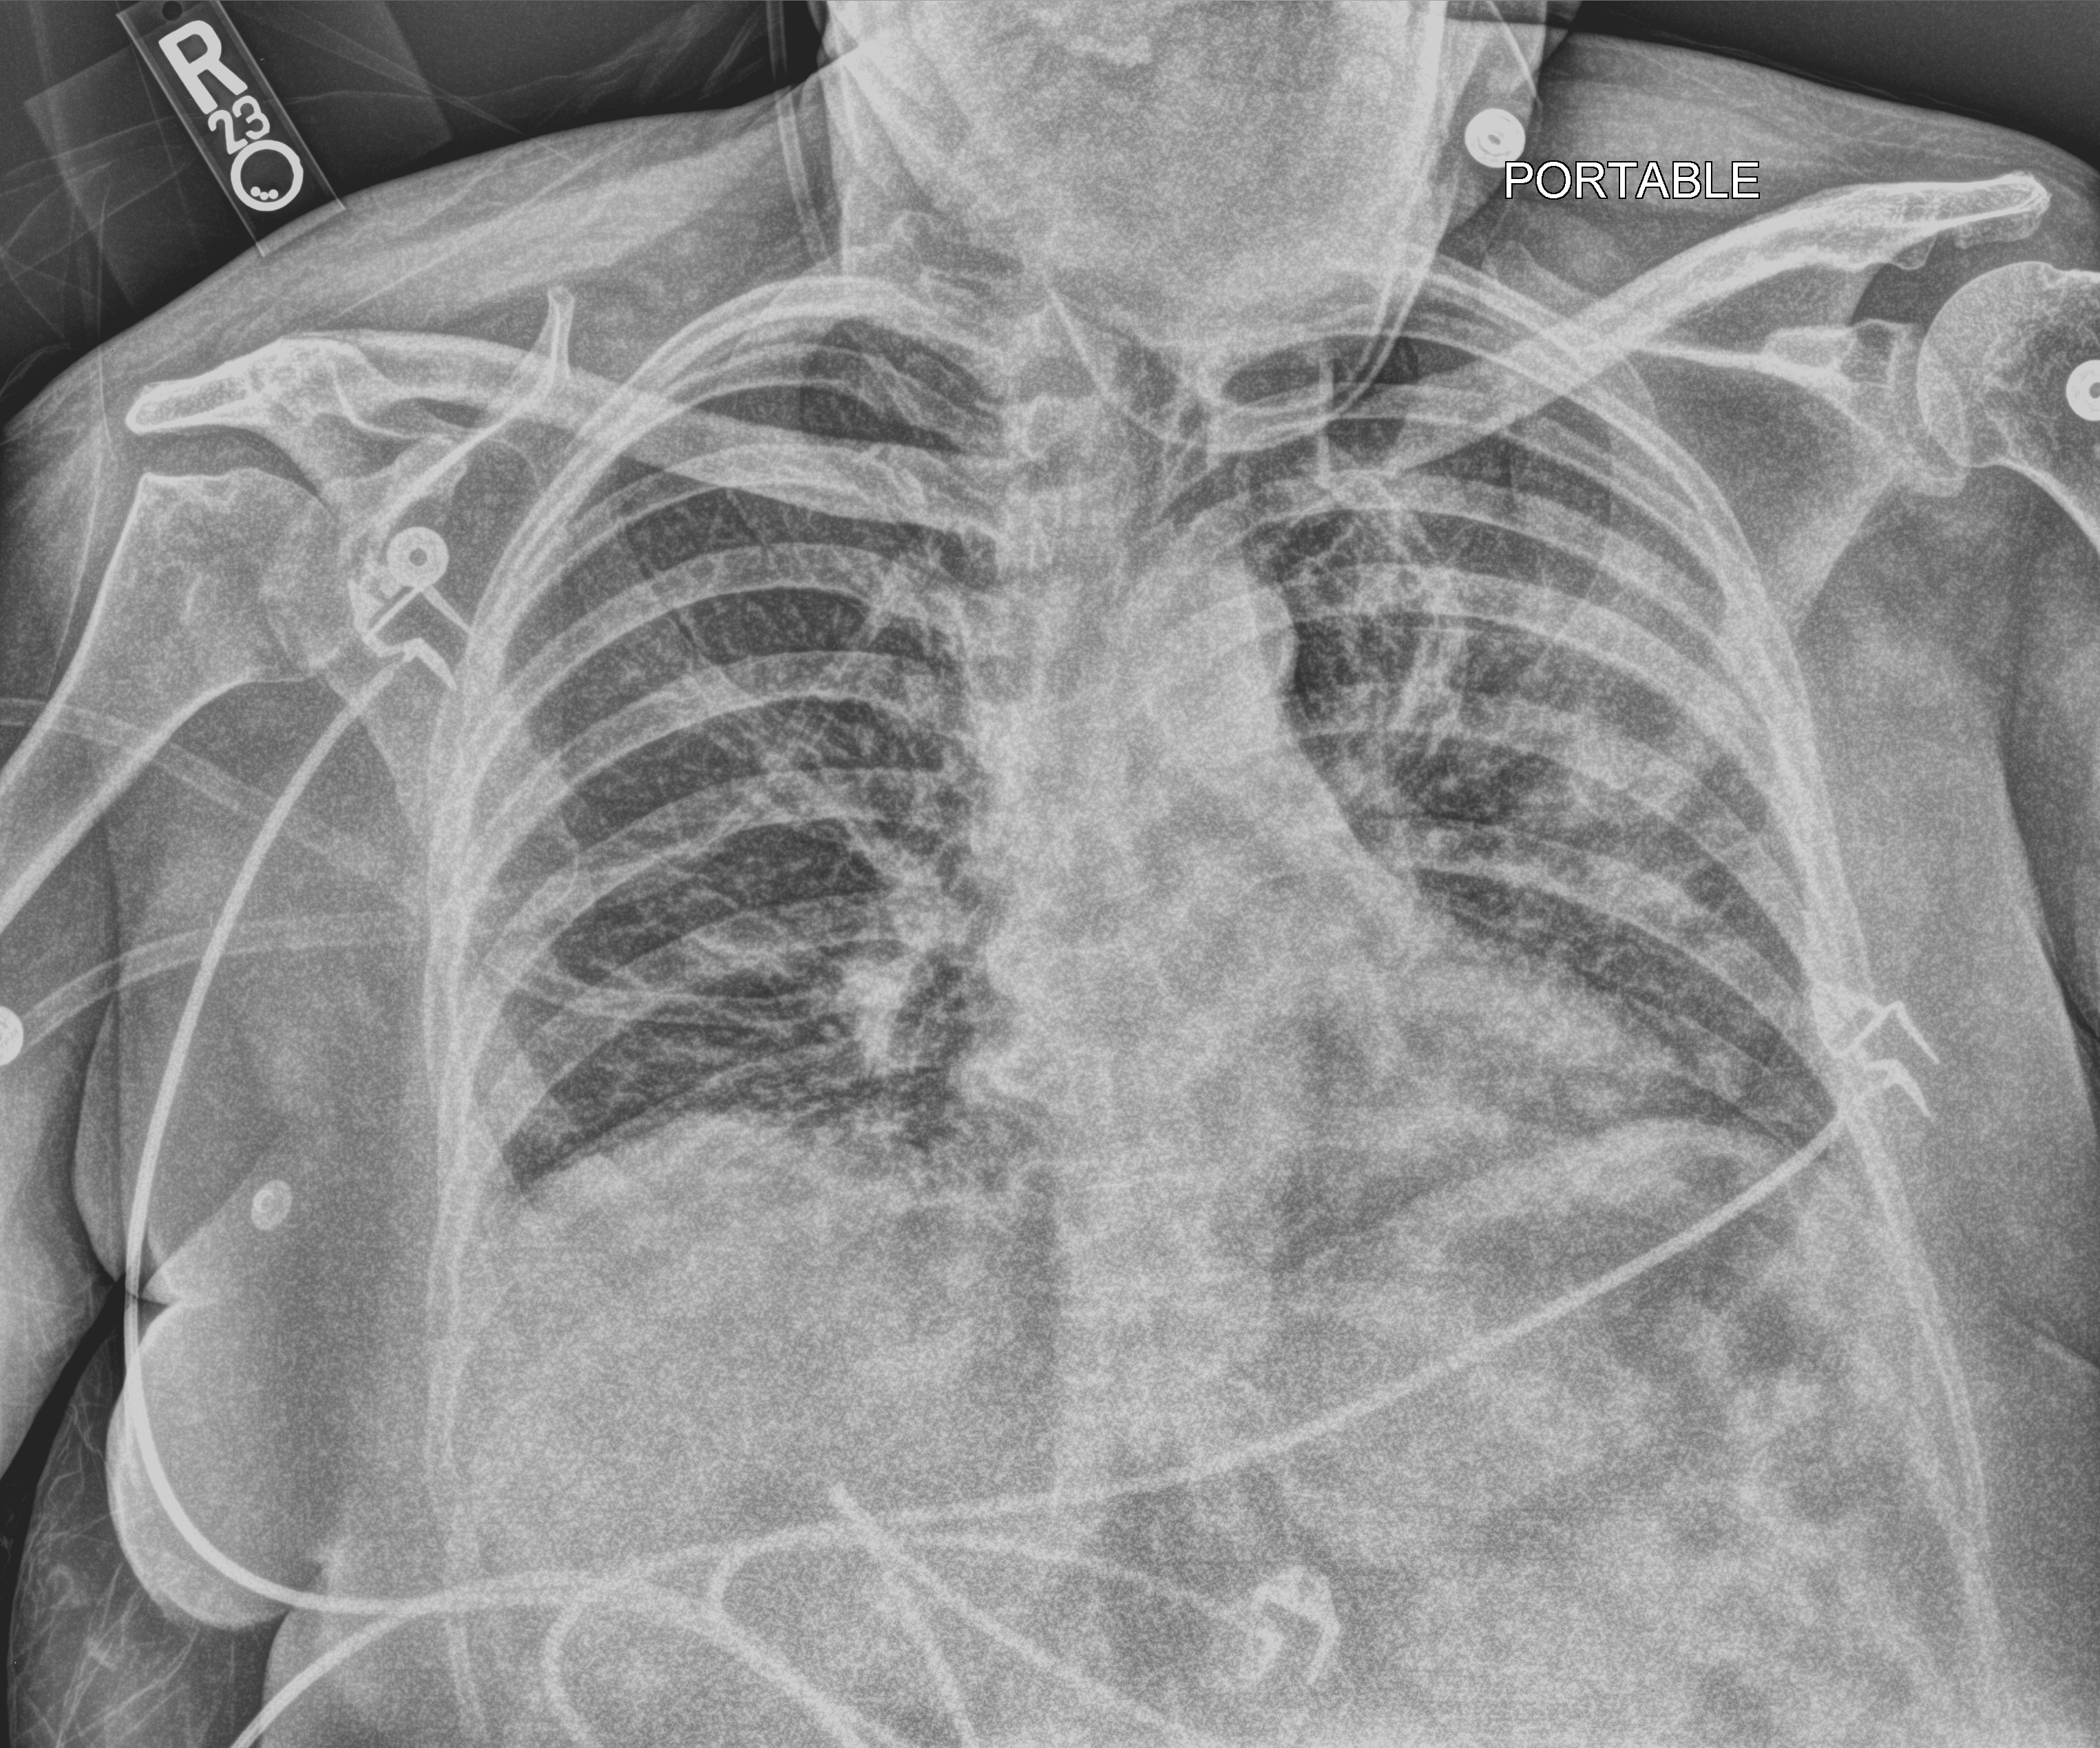
Portable chest radiograph. Female patient hospitalised with COVID-19, age 60–74 years.
Hospital-stay facts (about this admission, not read from this image; timing relative to this image not recorded):
- mechanically ventilated during this hospital stay: no